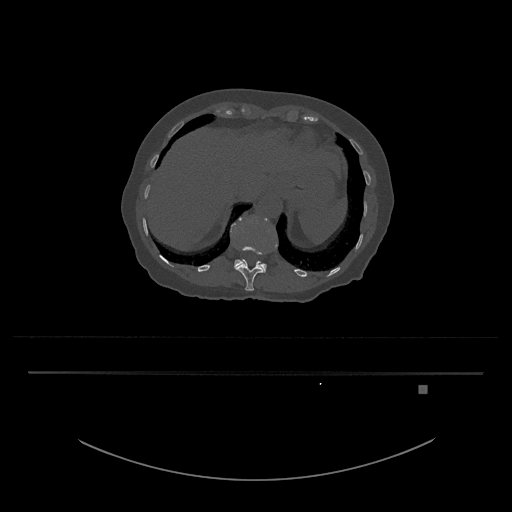
CT including the spine, one axial slice. Position 592 of 797 along the scan axis. Reconstruction kernel Br40s/3. Bone window (W 1800 / L 400 HU). 0.5 mm slice thickness. 512 × 512 image matrix, field of view 500 × 500 mm. Female patient, age 57 years. From the clinical record (not read from this slice): primary cancer: cervical.
Structures marked on this image (semi-automatic segmentation, software-assisted and operator-edited):
- L1 vertebra: box from (x=231, y=216) to (x=269, y=271) px
- T12 vertebra: (x=234, y=235)–(x=266, y=291)